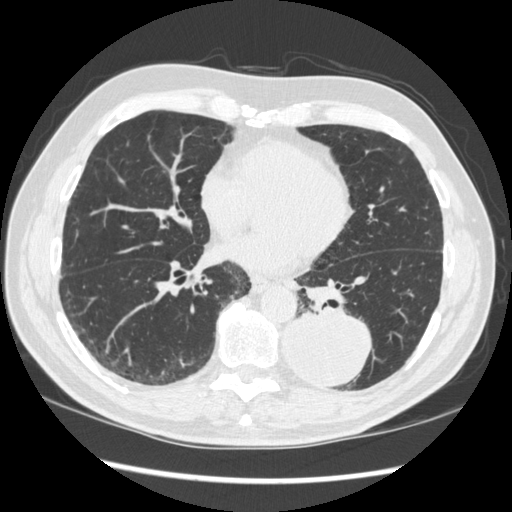
Chest CT (low-dose screening protocol), one axial image, baseline screening round, lung window (W 1500 / L -600 HU), 512 × 512 image matrix, field of view 360 × 360 mm. Male, age 72 years at enrolment. Current smoker at enrolment.
Expert reader's lesion annotation, bounding box (x1, y1, x2, y2) in pixels: (270, 300, 374, 390). The screening reader recorded 2 non-calcified nodules or masses ≥4 mm on this exam (left lower lobe, right middle lobe); which of them this box marks is not recorded. Official screen result: positive, change unspecified: nodule(s) >= 4 mm or enlarging nodule(s), mass(es), or other non-specific abnormalities suspicious for lung cancer. Participant outcome: lung cancer diagnosed 37 days after this screen — squamous cell carcinoma, NOS, left lower lobe, stage IIIA (AJCC 6th edition), 60 mm at pathology.